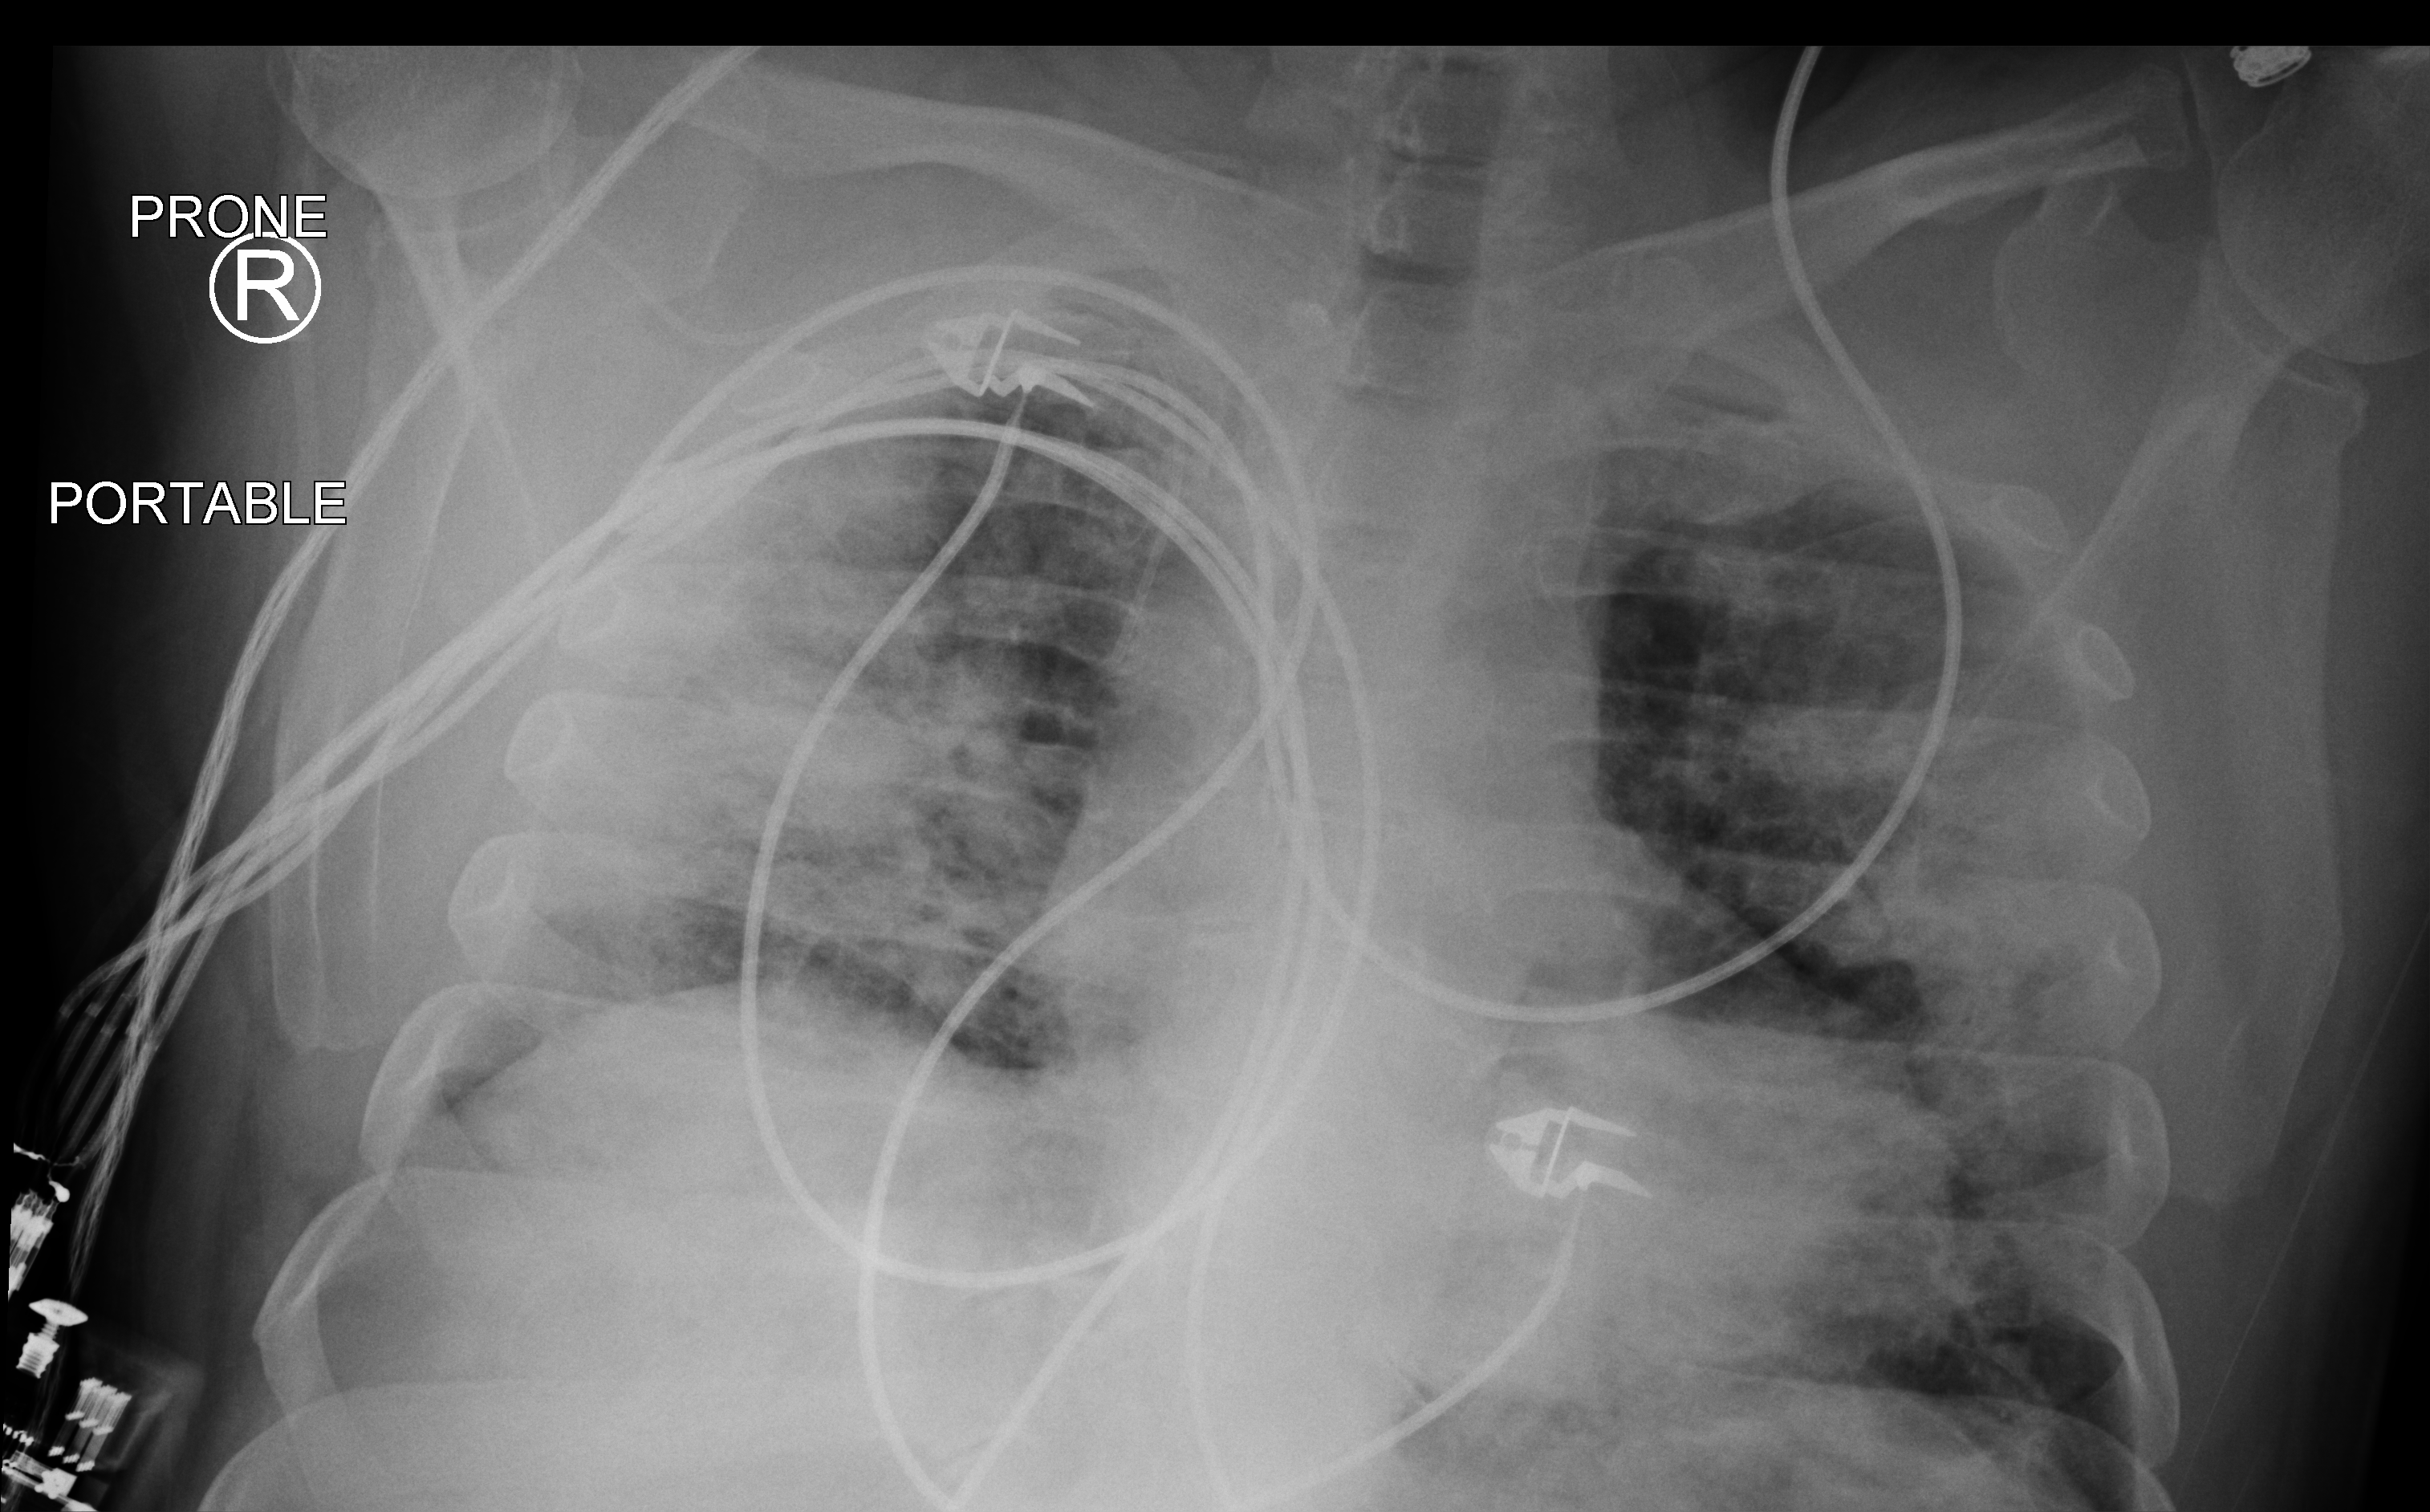
Bedside chest radiograph (computed radiography), posteroanterior (PA) projection. Male patient hospitalised with COVID-19, age 18–59 years.
Admission-level facts for this patient (not findings on this image; timing relative to this image not recorded):
- admitted to intensive care during this hospital stay: yes